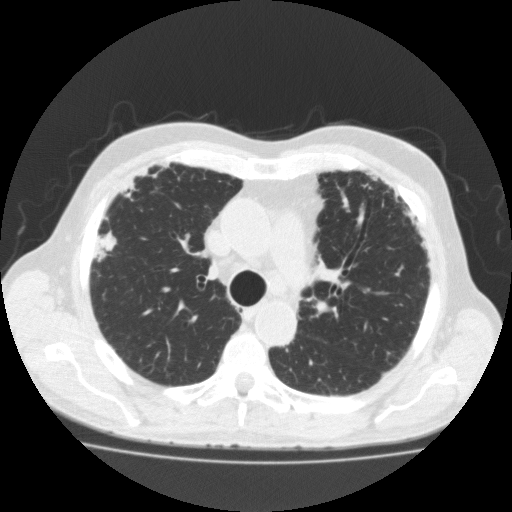
Low-dose screening chest CT, one axial slice; position 130 of 188 along the scan axis; 120 kVp; lung window (W 1500 / L -600 HU); 2 mm slice thickness; 512 × 512 image matrix.
Outlined on this slice (expert manual segmentation):
- lesion 1 (tumor, upper lobe of right lung): box from (x=100, y=233) to (x=117, y=252) px